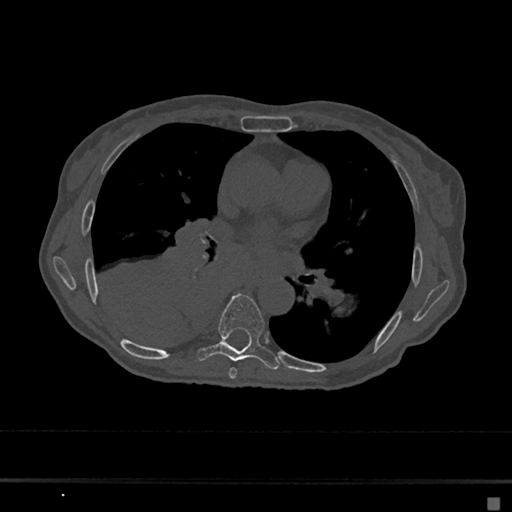
CT including the spine, one axial slice. Reconstruction kernel Br40s/3. 120 kVp. Bone window (W 1800 / L 400 HU). 0.5 mm slice thickness. 512 × 512 image matrix, field of view 360 × 360 mm. Female patient, age 68 years. Case-level facts recorded for this patient, not image findings: primary cancer: renal.
Annotated regions visible in this slice (semi-automatically segmented with operator editing):
- T6 vertebra: bounding box [x1, y1, x2, y2] px = [228, 367, 237, 379]
- T7 vertebra: [196, 294, 280, 370]